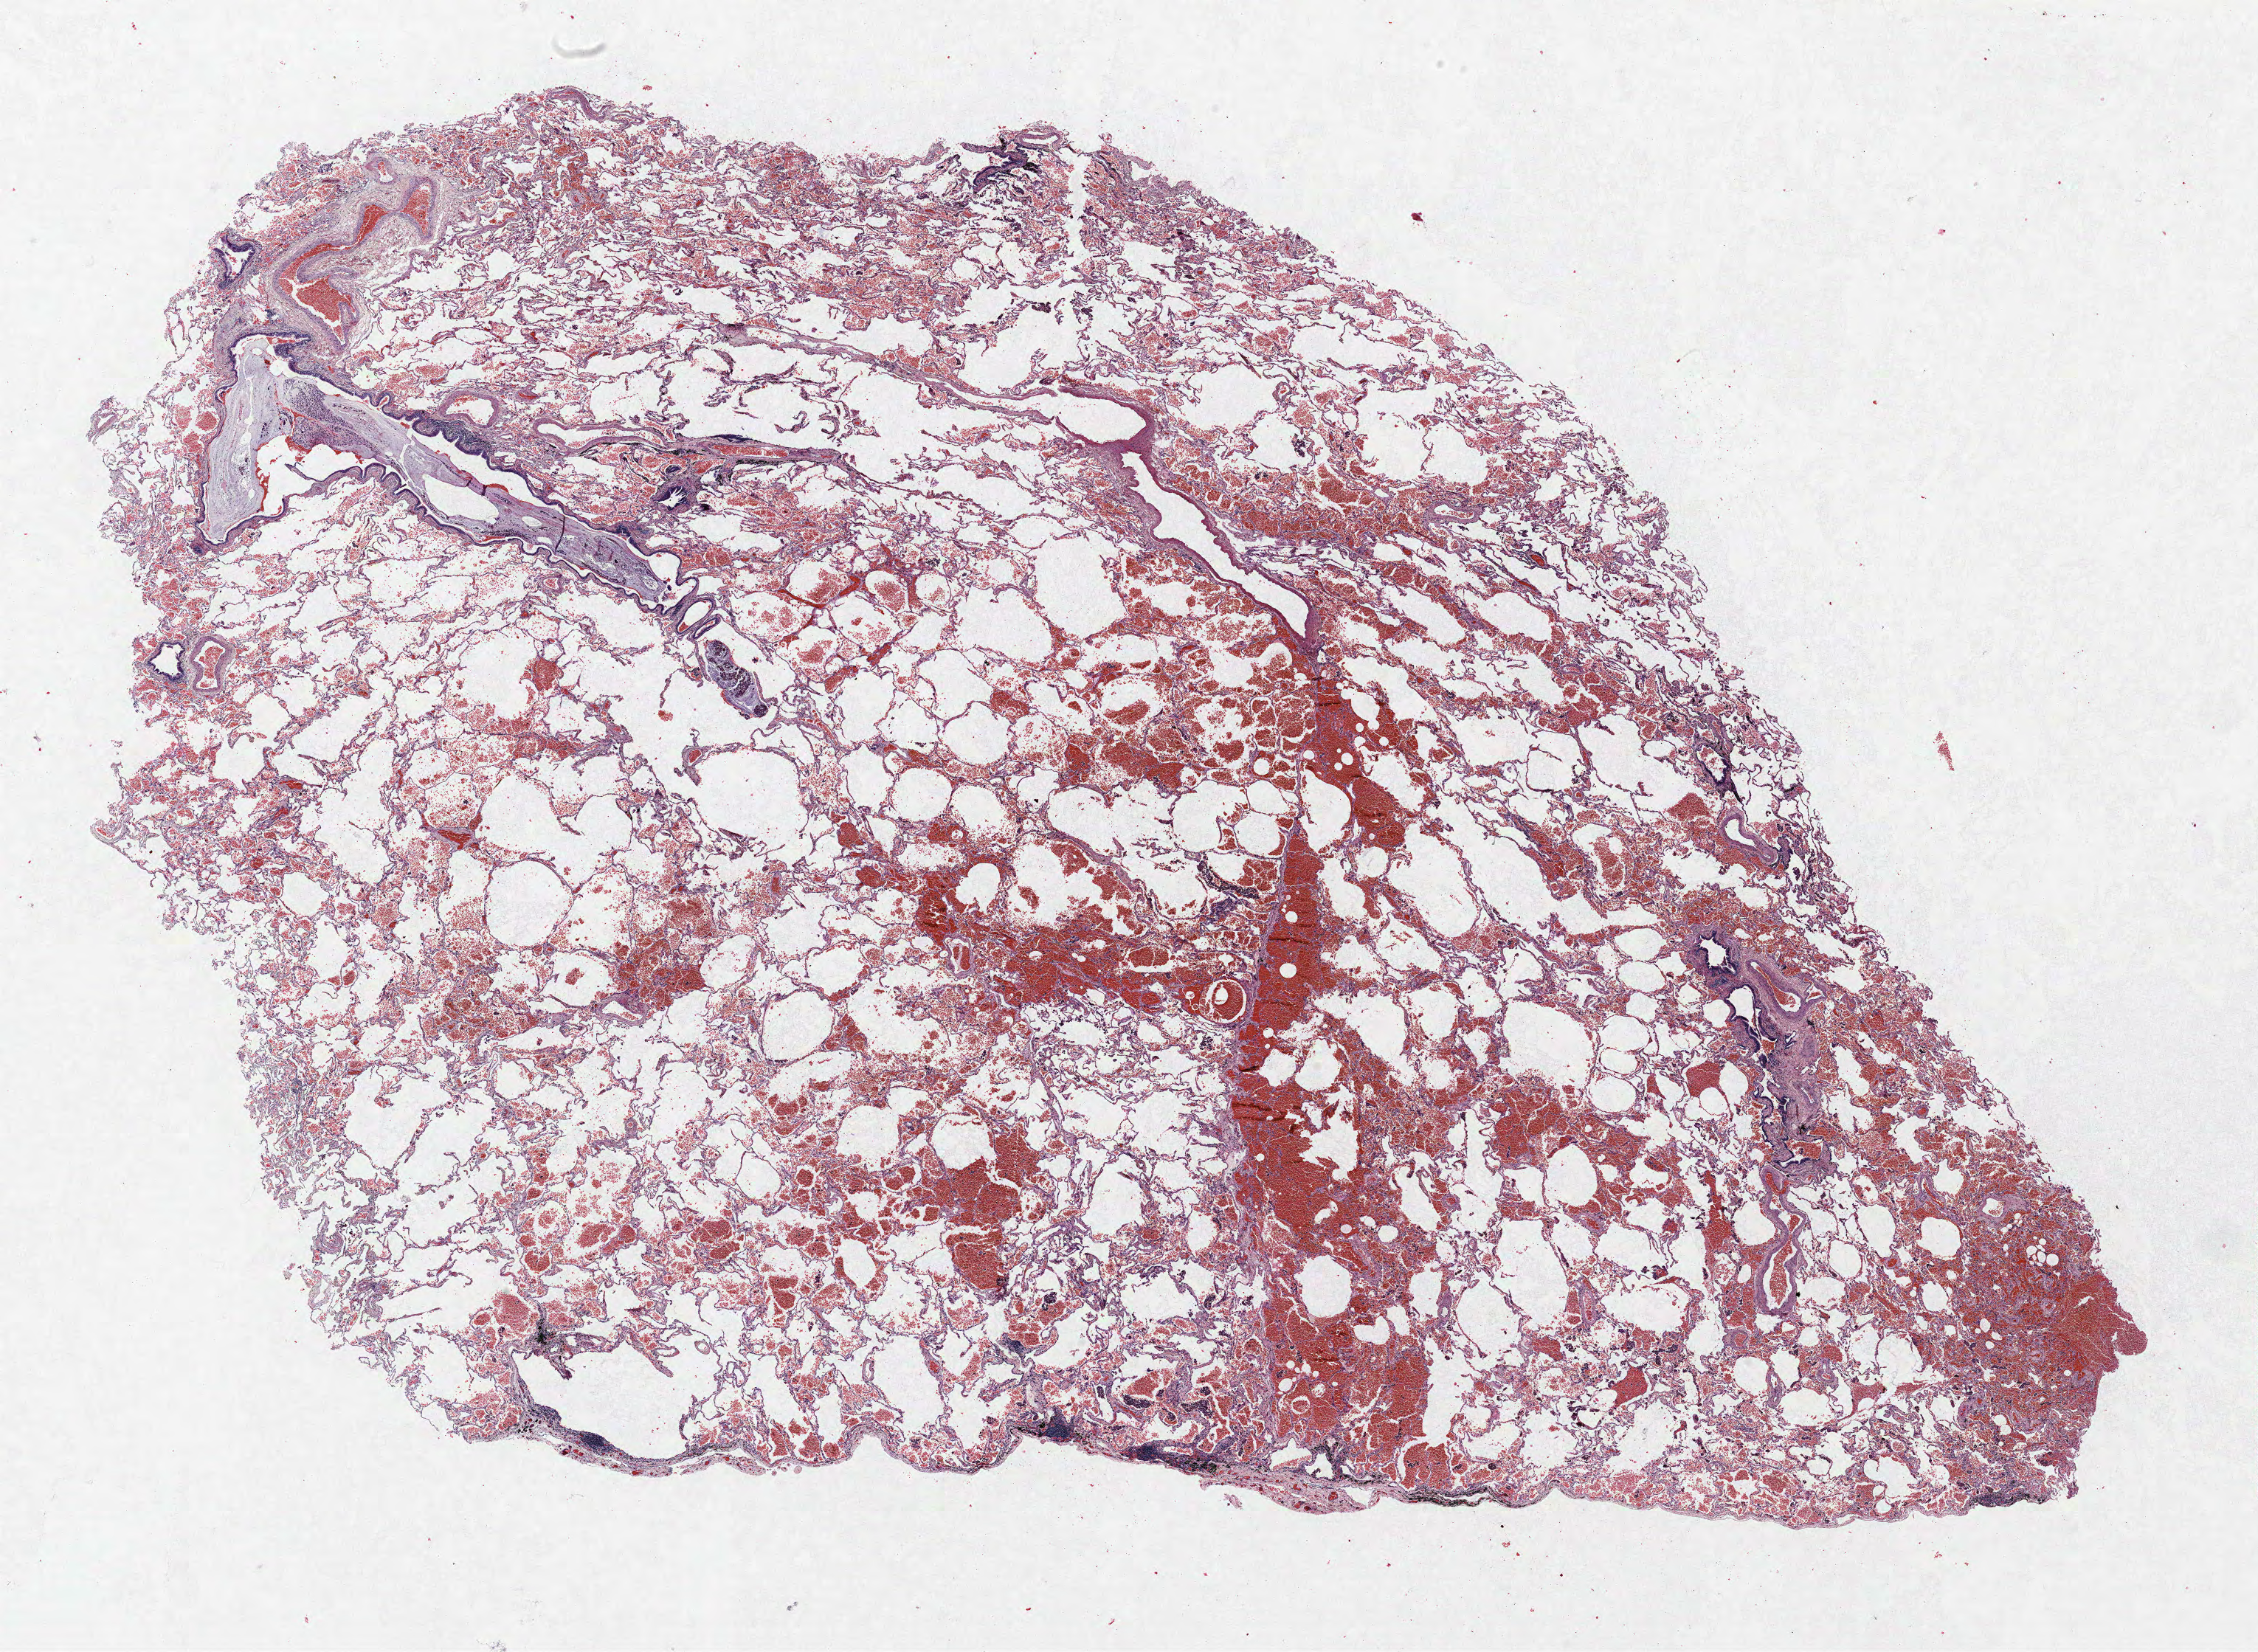
Whole-slide histology image, Hematoxylin and eosin (H&E) stained — a low-resolution overview of the entire scanned area, about 24.5 x 17.9 mm. Formalin-fixed paraffin-embedded (FFPE) section. Lung tissue. Male patient, aged 72 at enrolment.
Participant's lung-cancer diagnosis: Mucin-producing adenocarcinoma (ICD-O-3 8481/3).